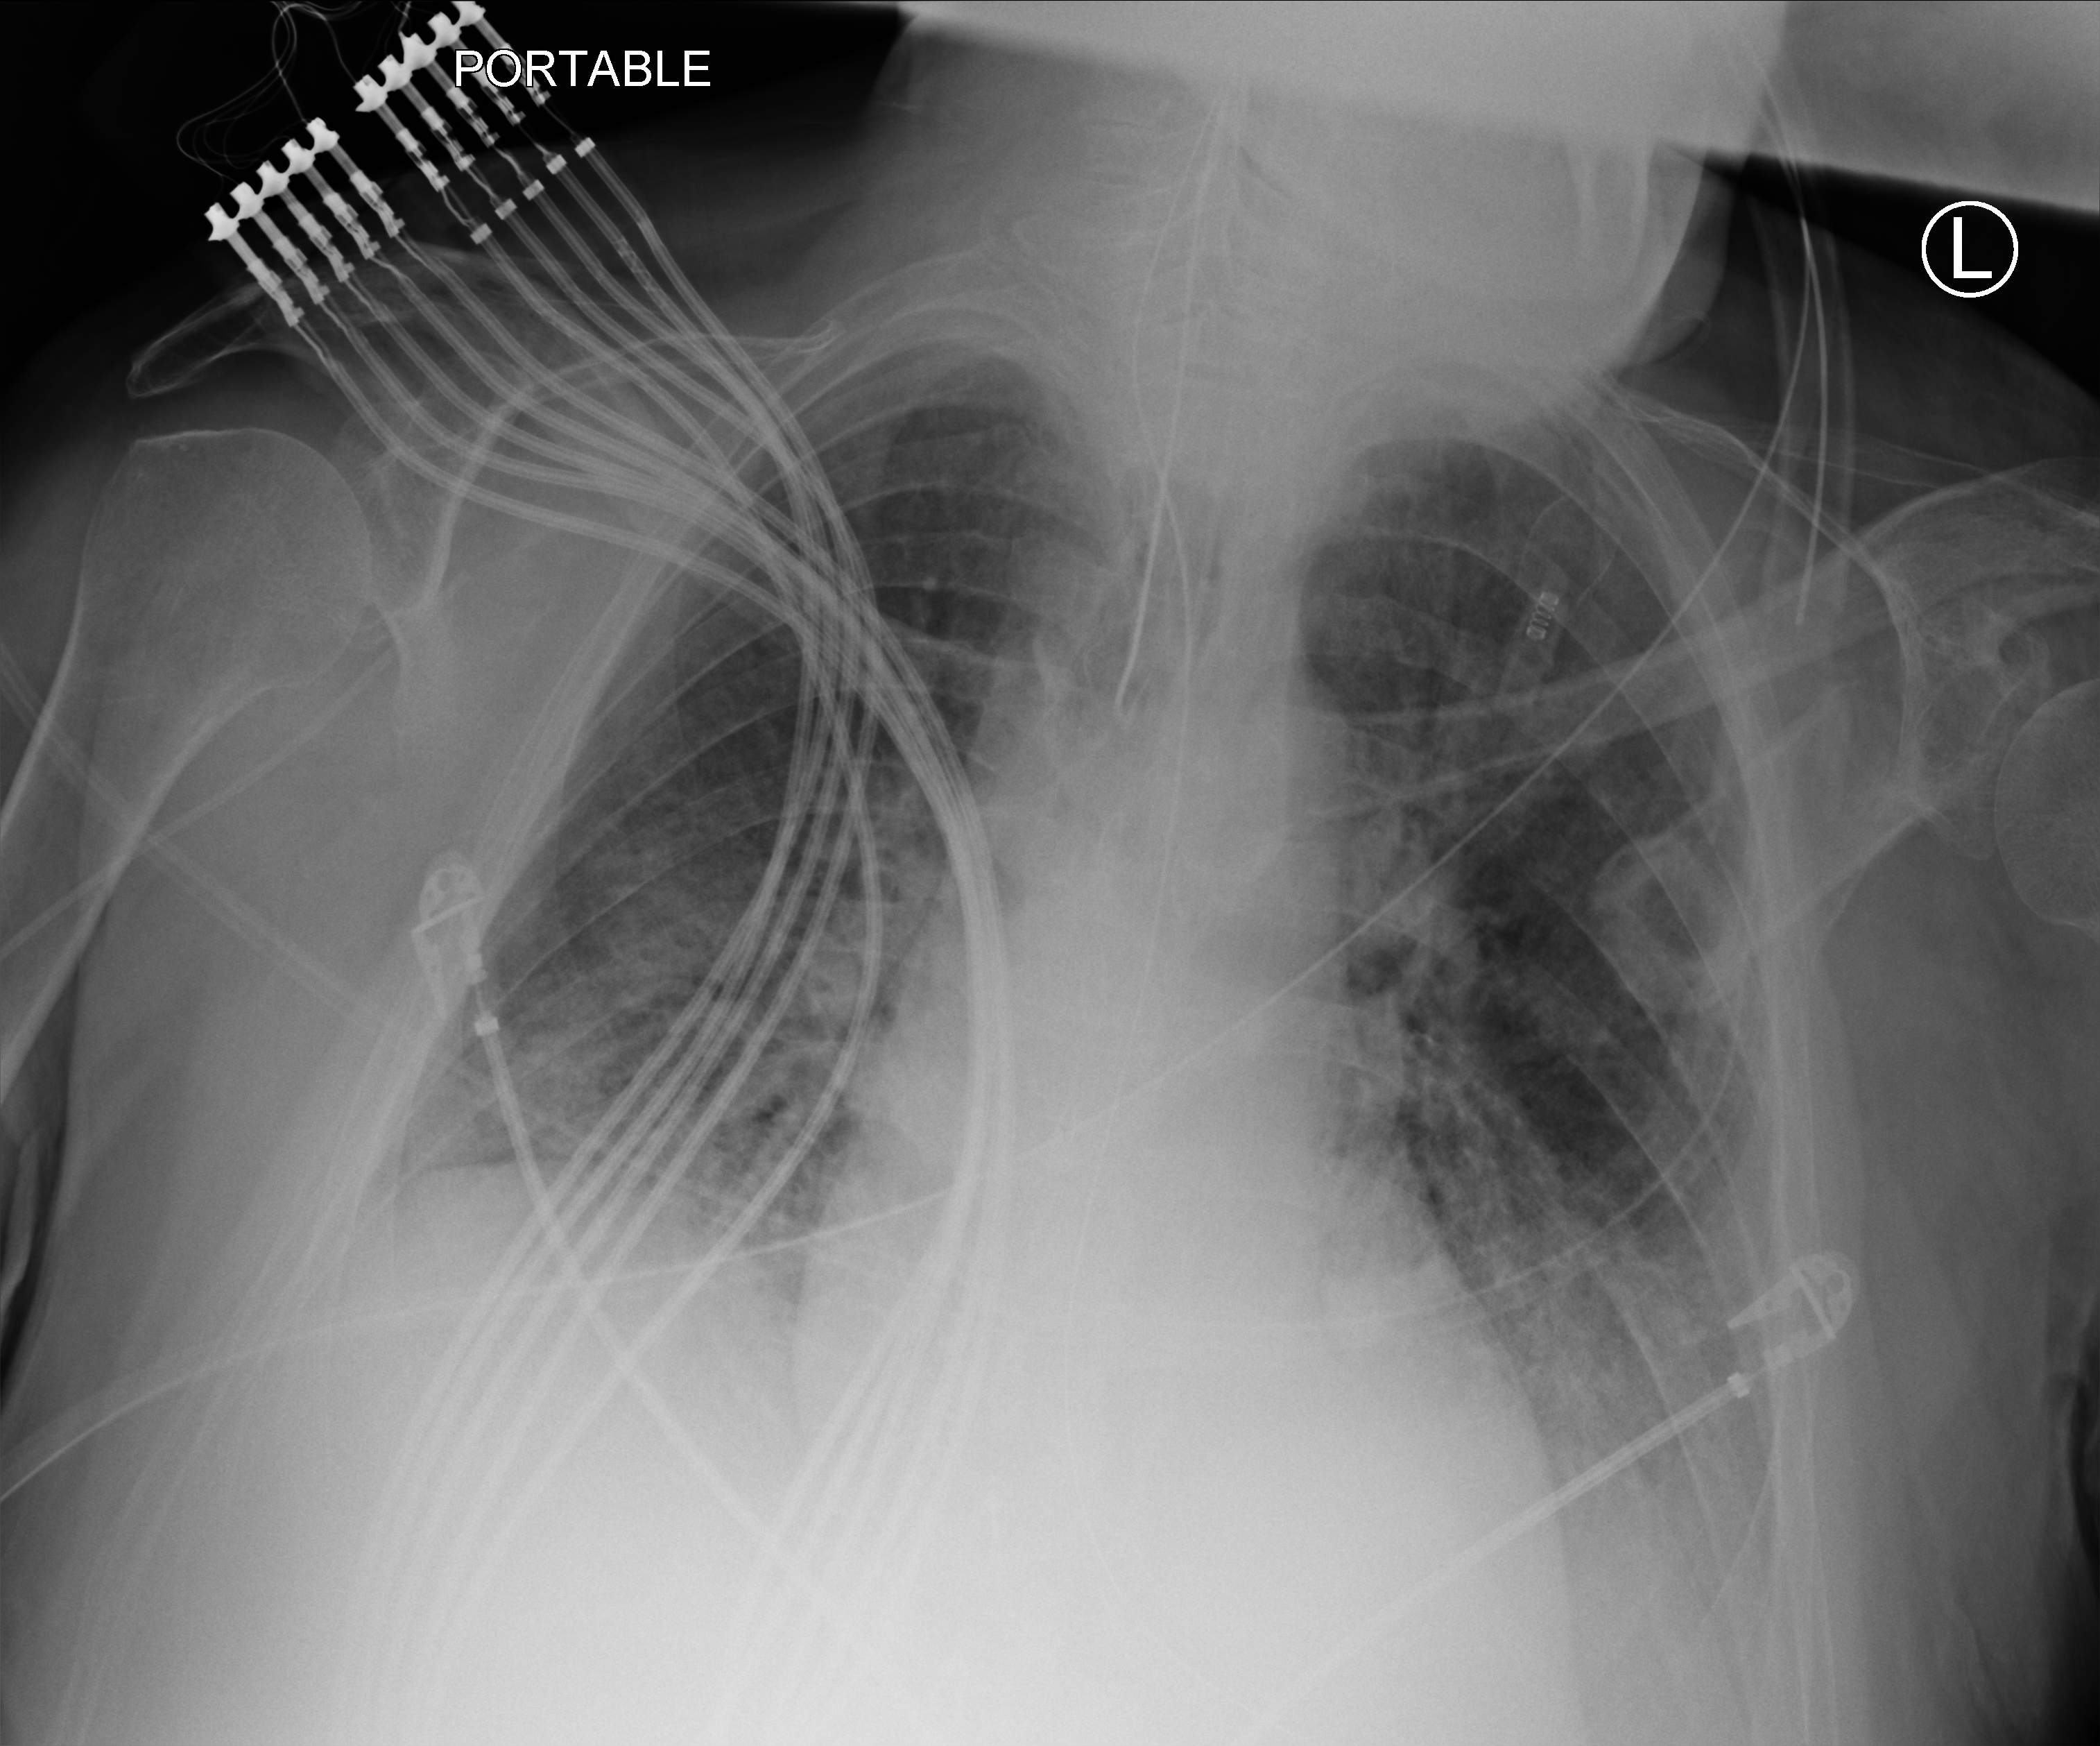
Portable chest radiograph; anteroposterior (AP) projection. Male patient hospitalised with COVID-19, age 60–74 years.
From the hospital-stay record, not from the radiograph (when in the stay this image was taken is not recorded): hypertension (admission record): no; mechanically ventilated during this hospital stay: yes.